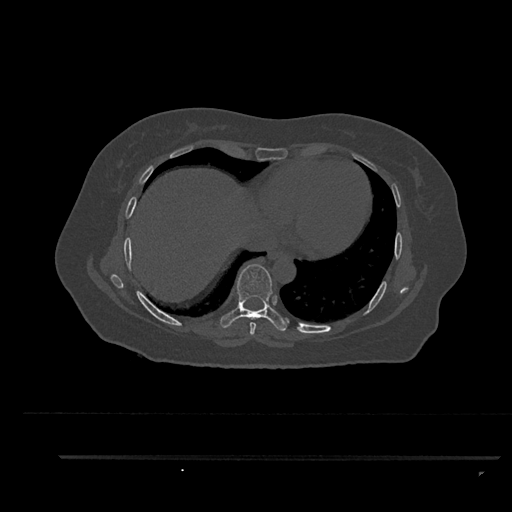
CT including the spine, one axial slice; slice 469 of 797 in the series (ordered by position); bone window (W 1800 / L 400 HU); 512 × 512 image matrix. Patient: female, 44 years. Case-level facts recorded for this patient, not image findings: primary cancer: renal; vertebrae with lytic lesions (as recorded): L1.
Annotated regions visible in this slice (semi-automatically segmented with operator editing):
- T7 vertebra: bounding box <250,322,256,335> (left, top, right, bottom; pixels)
- T8 vertebra: <220,264,287,331>